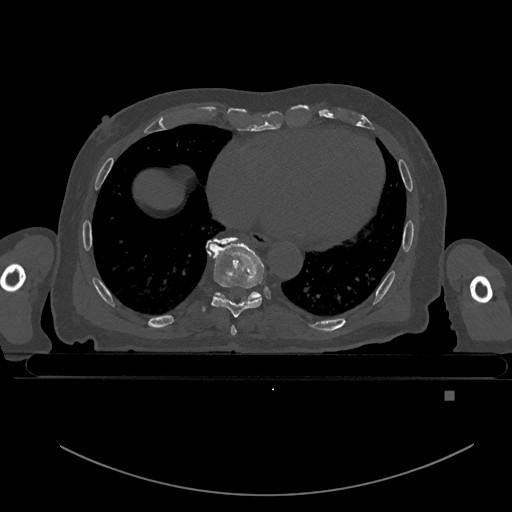
CT including the spine, one axial slice; slice 191 of 969 in the series (ordered by position); bone window (W 1800 / L 400 HU); 512 × 512 image matrix, field of view 456 × 456 mm. Male patient, age 82 years. From the clinical record (not read from this slice): primary cancer: prostate.
Annotated regions visible in this slice (semi-automatically segmented with operator editing):
- T7 vertebra: box from (x=231, y=325) to (x=237, y=336) px
- T8 vertebra: (x=201, y=239)–(x=264, y=318)
- T9 vertebra: (x=206, y=237)–(x=261, y=301)